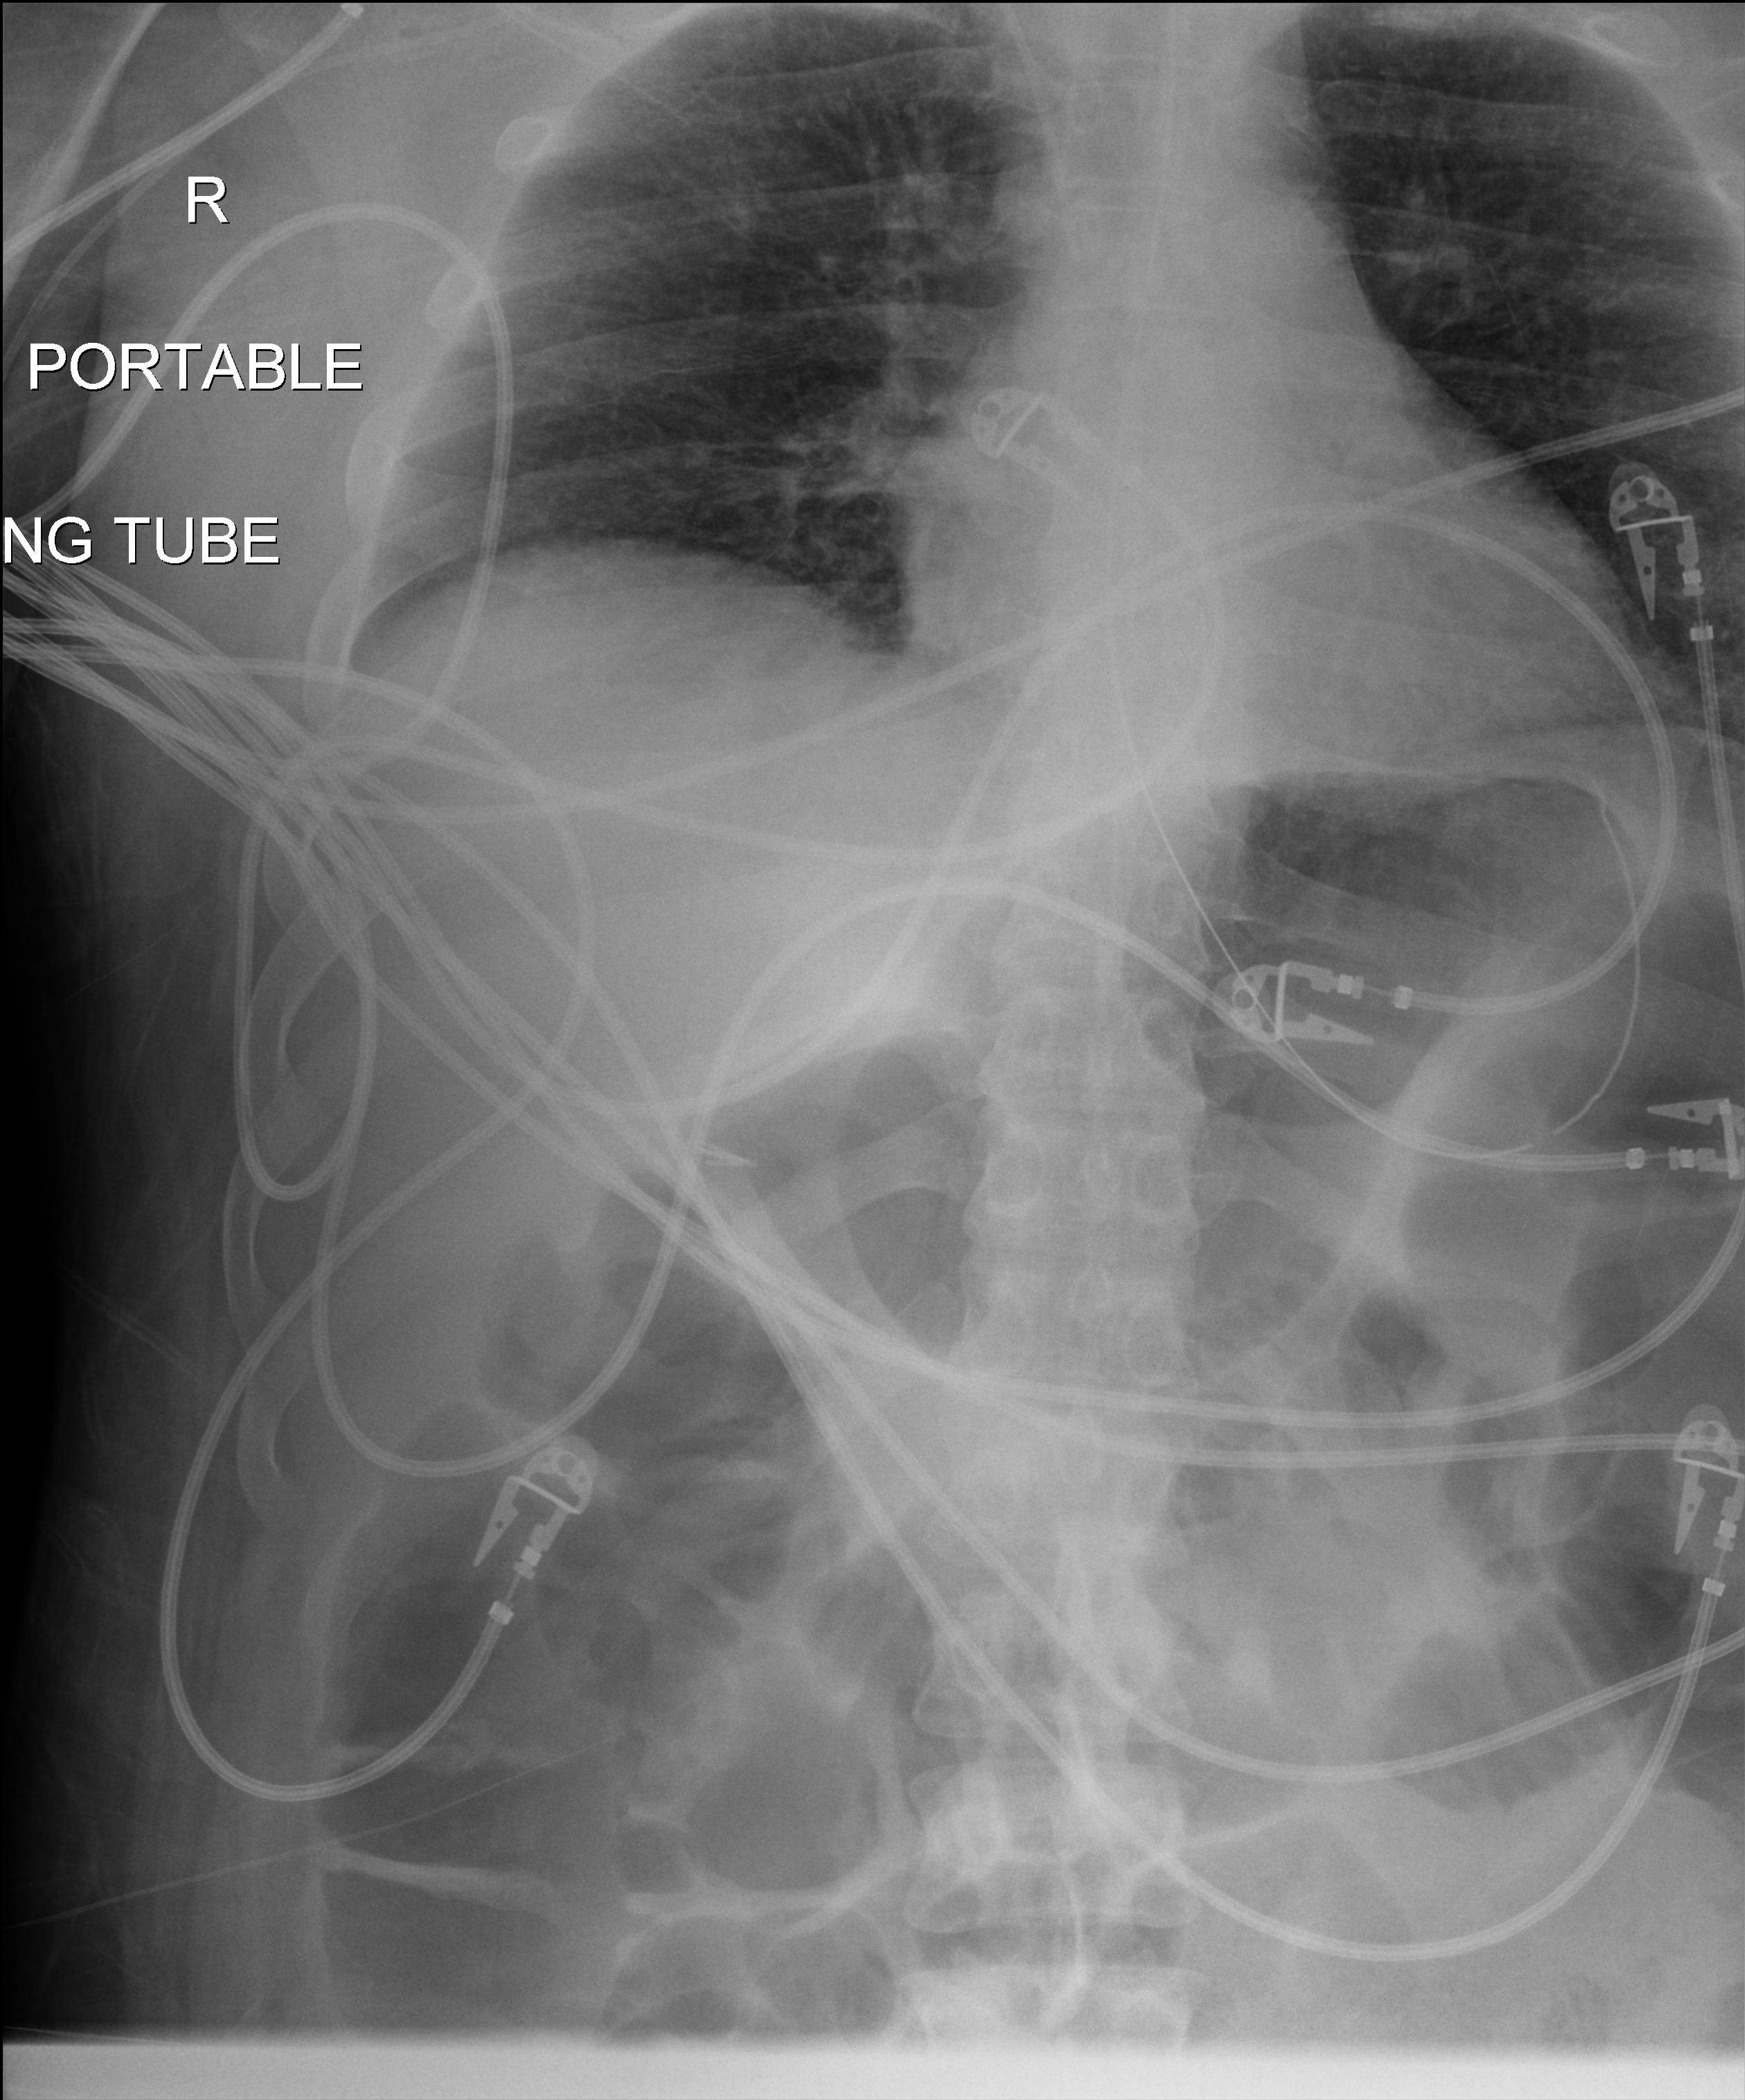
Chest X-ray (portable), anteroposterior (AP) projection. Patient hospitalised with COVID-19; male, aged 18–59 years.
From the hospital-stay record, not from the radiograph (when in the stay this image was taken is not recorded): length of hospital stay: 44 days; COPD (admission record): no; smoking status (admission record): former.